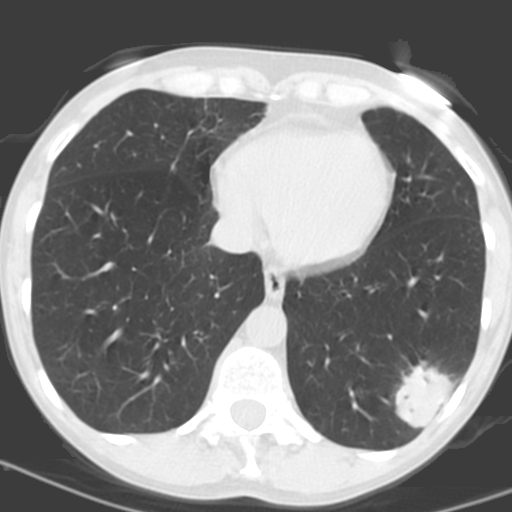
Axial slice from a low-dose chest CT screening exam; baseline annual screen; lung window (W 1500 / L -600 HU); 3.2 mm slice thickness; standard (soft-tissue) reconstruction kernel (C); slice 107 of 156 in the series; 512 × 512 image matrix. Female participant, aged 56 years at enrolment. Current smoker at enrolment.
• Lesion marked by an expert reader, box from (x=384, y=360) to (x=462, y=430) px.
• Screening reader's record for this exam (one nodule recorded; not confirmed to be the boxed lesion): non-calcified nodule or mass ≥4 mm, left lower lobe, 31 × 23 mm, poorly defined margins, soft tissue attenuation, pre-existing on the prior screen: no.
• Later outcome: lung cancer diagnosed 27 days after this screen — squamous cell carcinoma, NOS, left lower lobe, poorly differentiated (G3), stage IB (AJCC 6th edition), 35 mm at pathology.